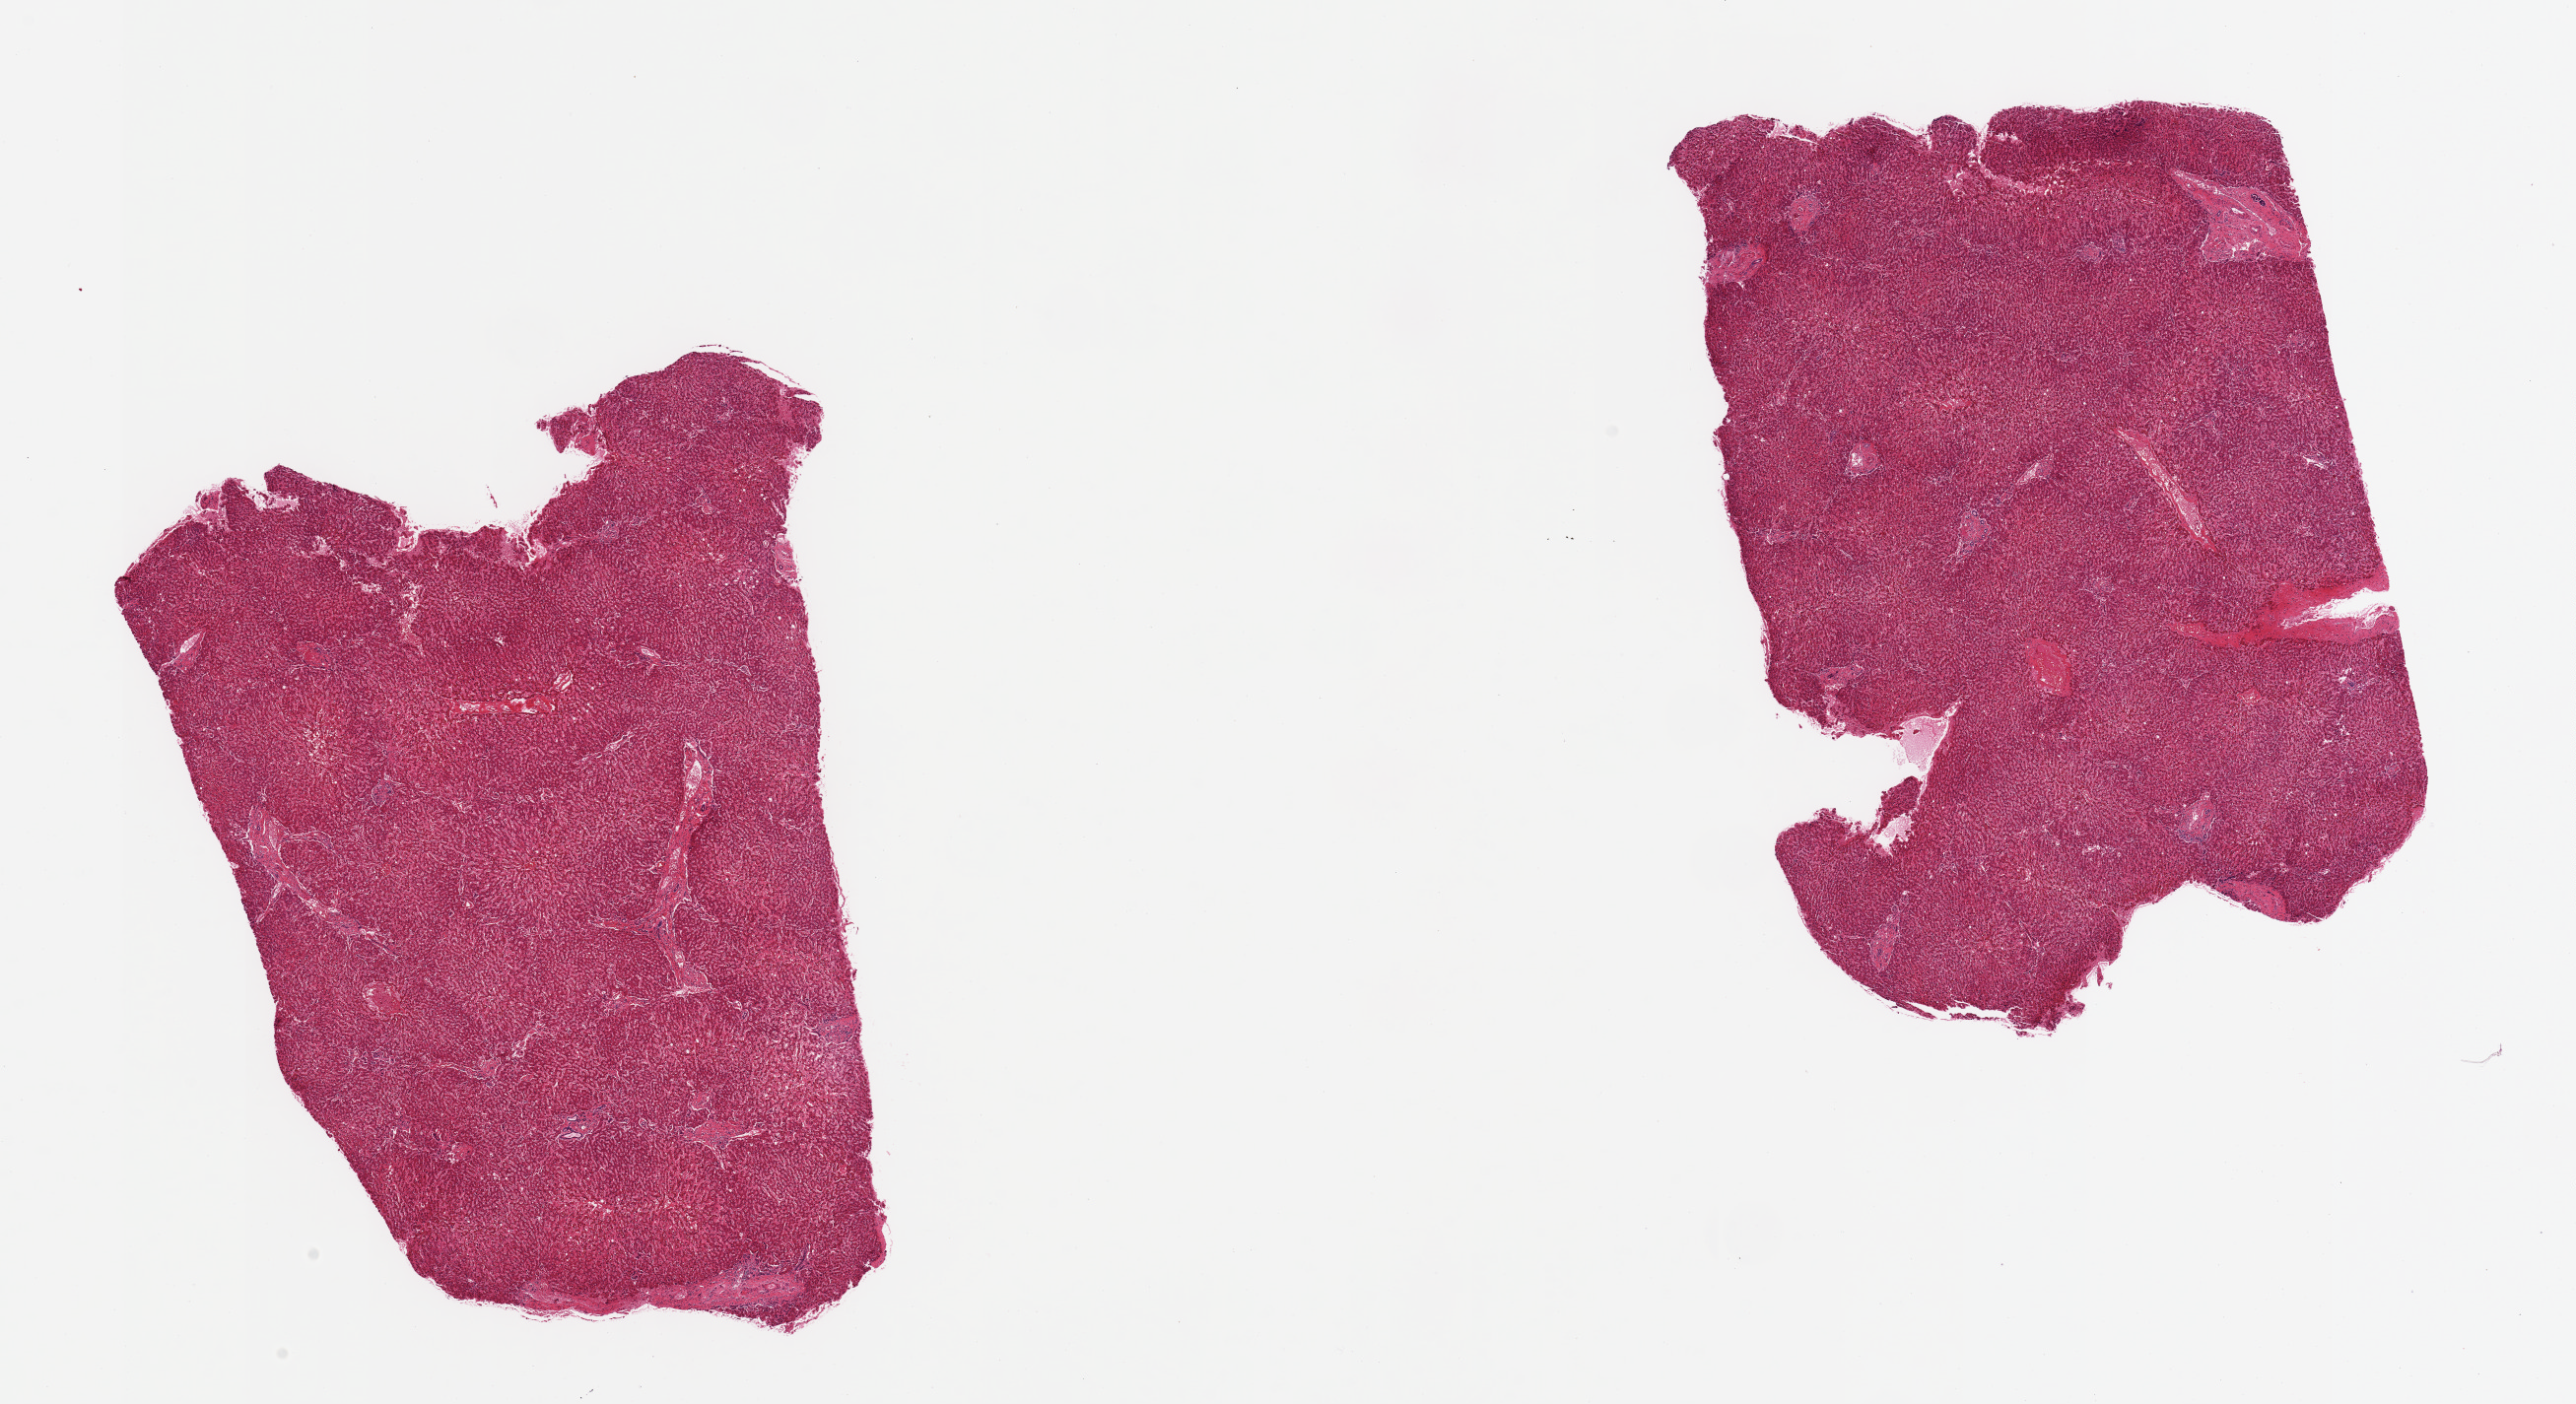
Whole-slide image, haematoxylin and eosin stain, whole scanned area (about 20.7 x 11.3 mm) shown as a low-resolution overview. PAXgene-fixed, paraffin-embedded tissue. Sampled site (target tissue): liver. Tissue donor sample. Female donor.
Reviewer comment on this tissue sample: 2 pieces; mild macrovesicular steatosis no inflammation or fibrosis.